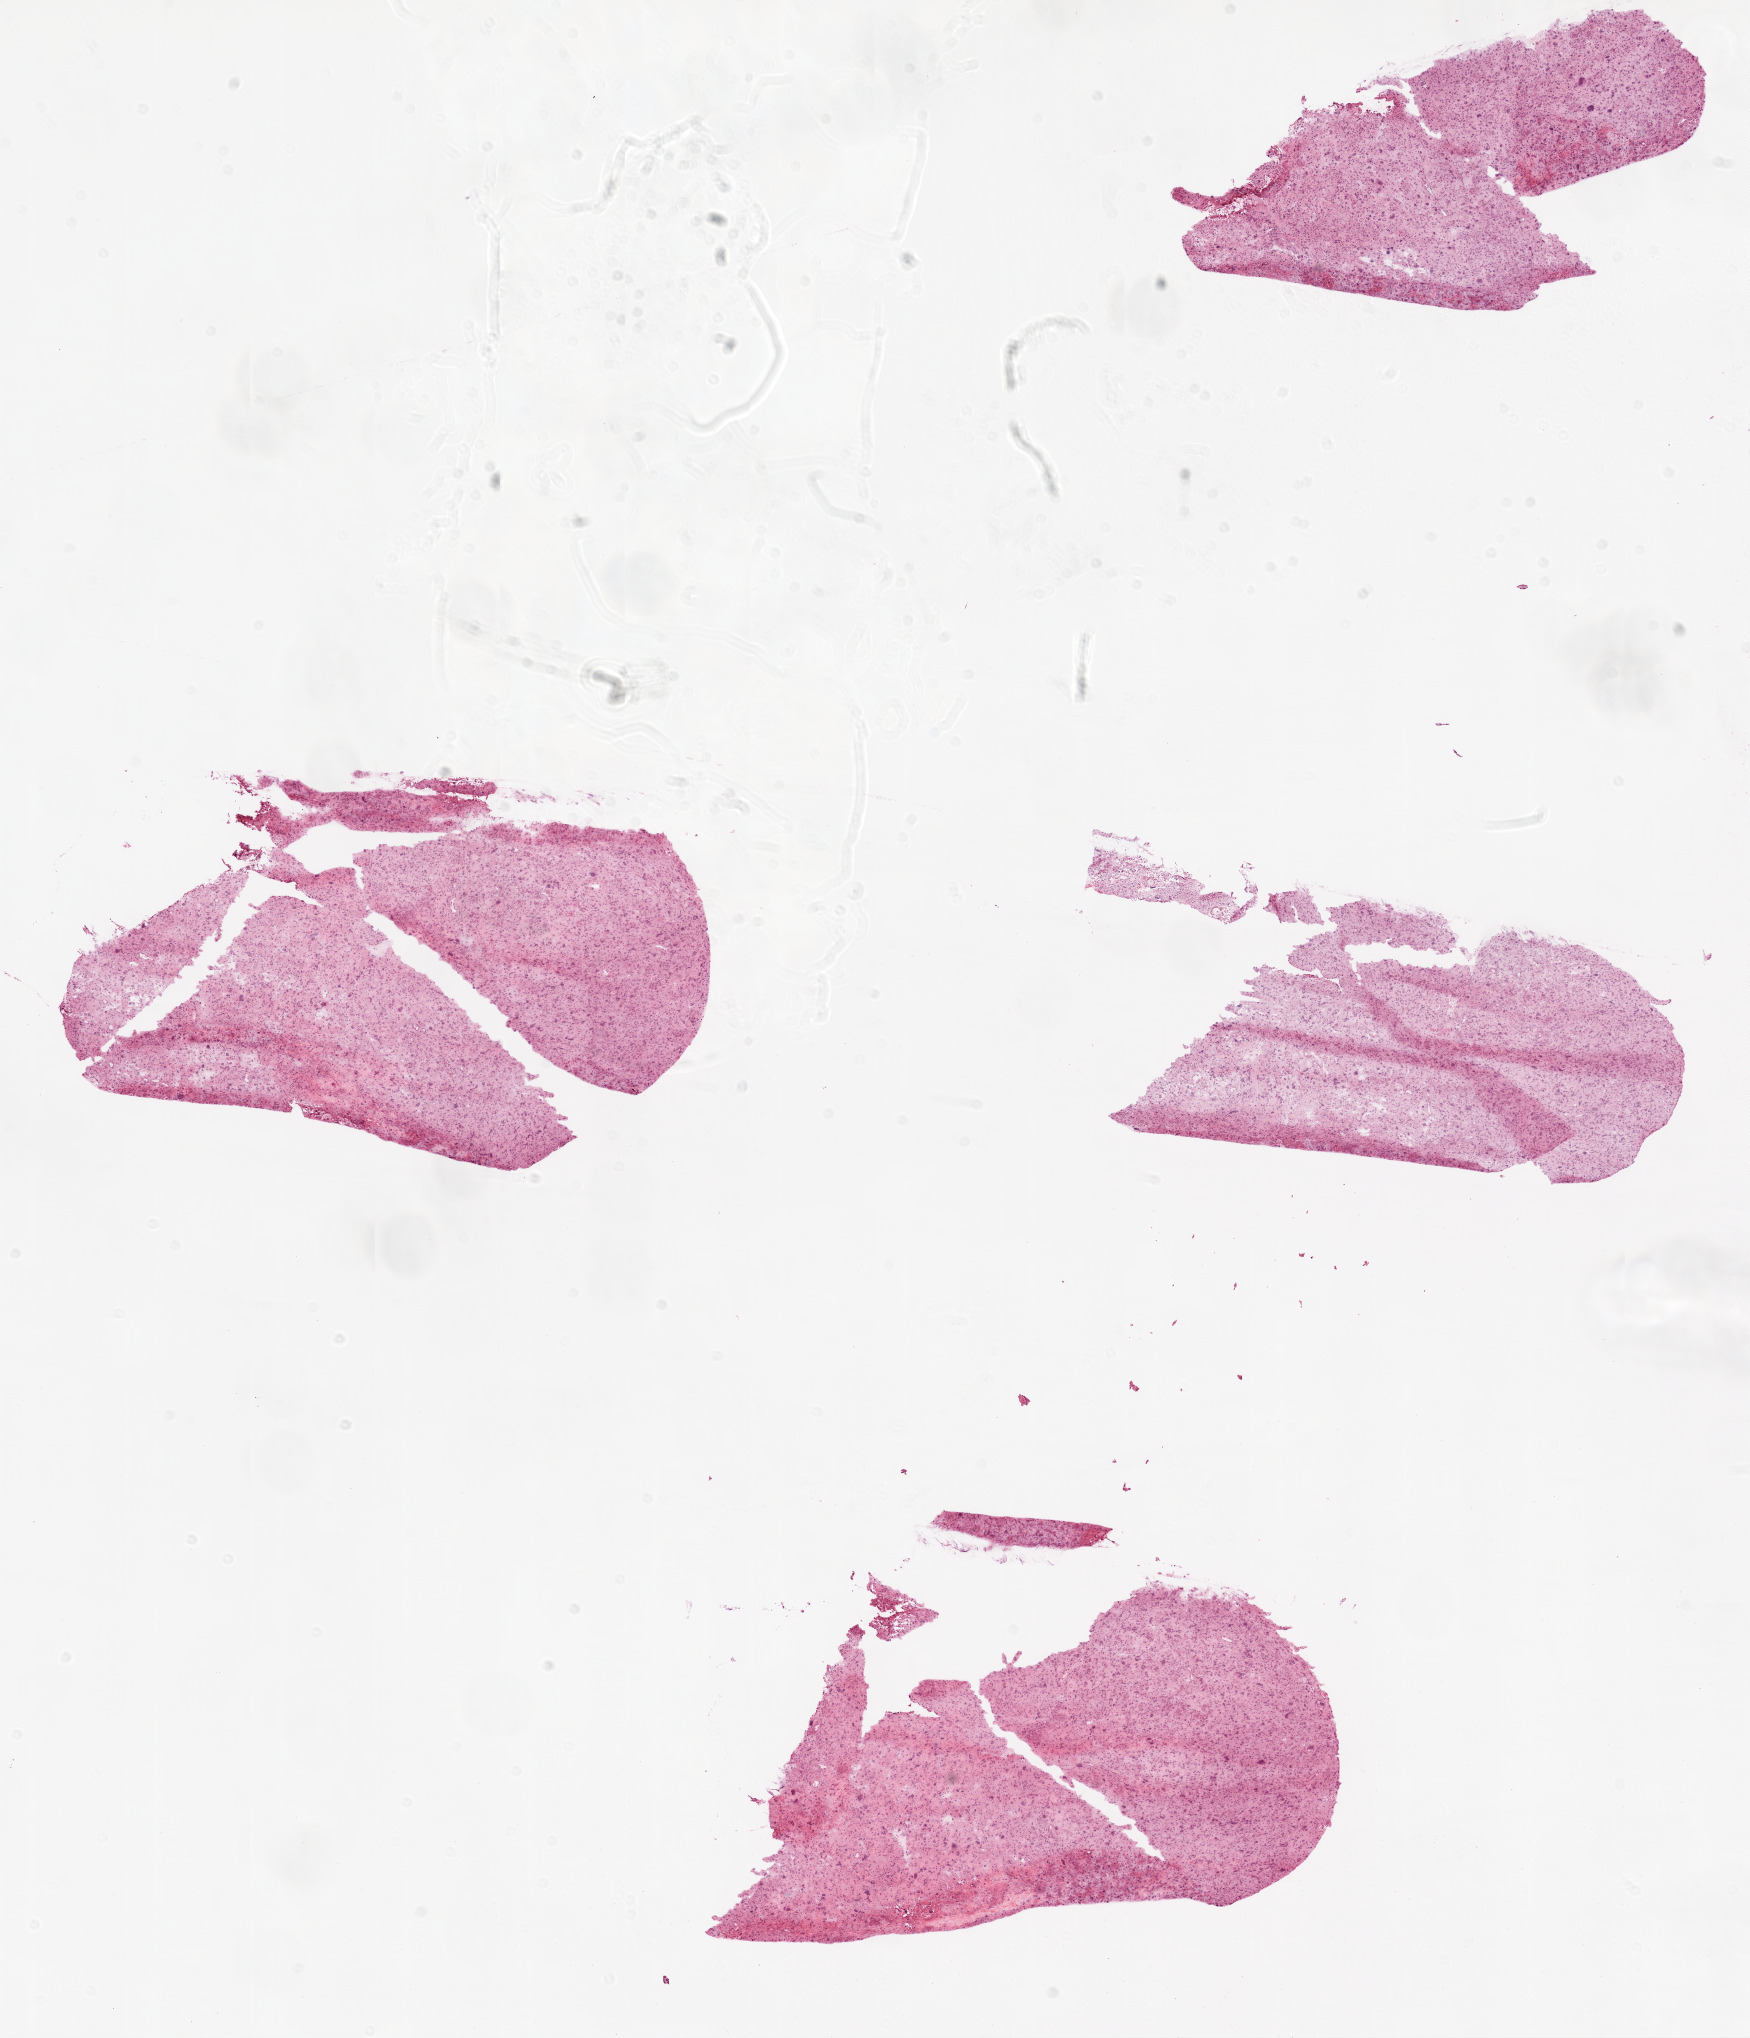
H&E-stained whole-slide image, low-resolution overview of the scanned area, about 14.0 x 16.4 mm; frozen section; primary tumour sample from the brain. Patient: female, age at initial diagnosis 53 years. Slide review estimates, as recorded: tumour cells 80%, tumour nuclei 85%, normal cells 10%, stromal cells 10%, necrosis 0%.
Histologic diagnosis: Glioblastoma.